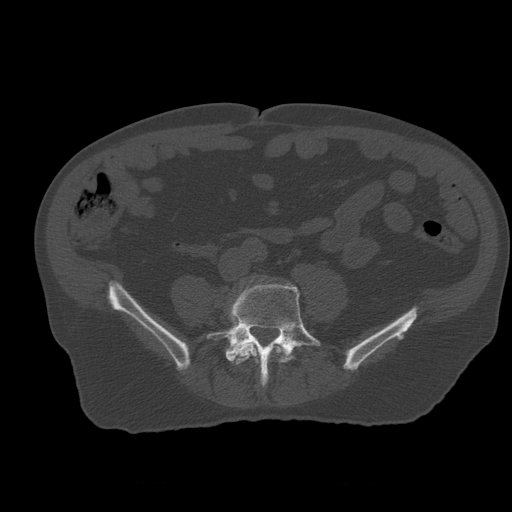
CT including the spine, one axial slice. Position 148 of 399 along the scan axis. Reconstruction kernel STANDARD. Bone window (W 1800 / L 400 HU). 1.25 mm slice thickness. 512 × 512 image matrix. Patient age 73 years. From the clinical record (not read from this slice): primary cancer: prostate.
Outlined on this slice (semi-automatic segmentation, software-assisted and operator-edited):
- L4 vertebra: bounding box [x1, y1, x2, y2] px = [233, 343, 288, 383]
- L5 vertebra: [207, 284, 321, 385]